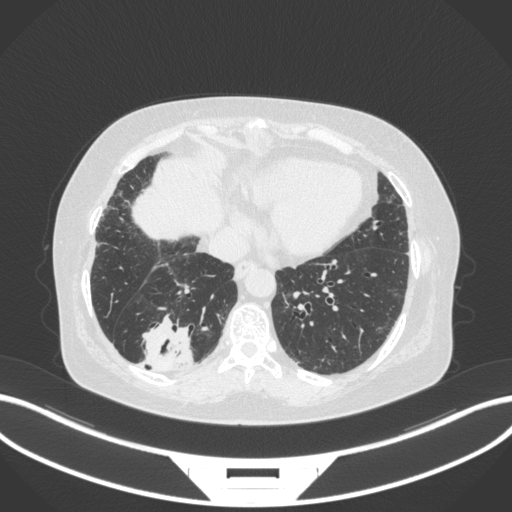
Chest CT, one axial slice. Slice 60 of 303 in the series (ordered by position). Reconstruction kernel B31f. Lung window (W 1500 / L -600 HU). 1 mm slice thickness. 512 × 512 image matrix, field of view 400 × 400 mm. Patient: female, 65 years. Case-level facts recorded for this patient, not image findings: clinical TNM (as recorded): T2b N1 M0.
Structures marked on this image (bounding box drawn by a radiologist):
- lung tumour (recorded histology: adenocarcinoma): bounding box [x1, y1, x2, y2] px = [138, 311, 196, 375]